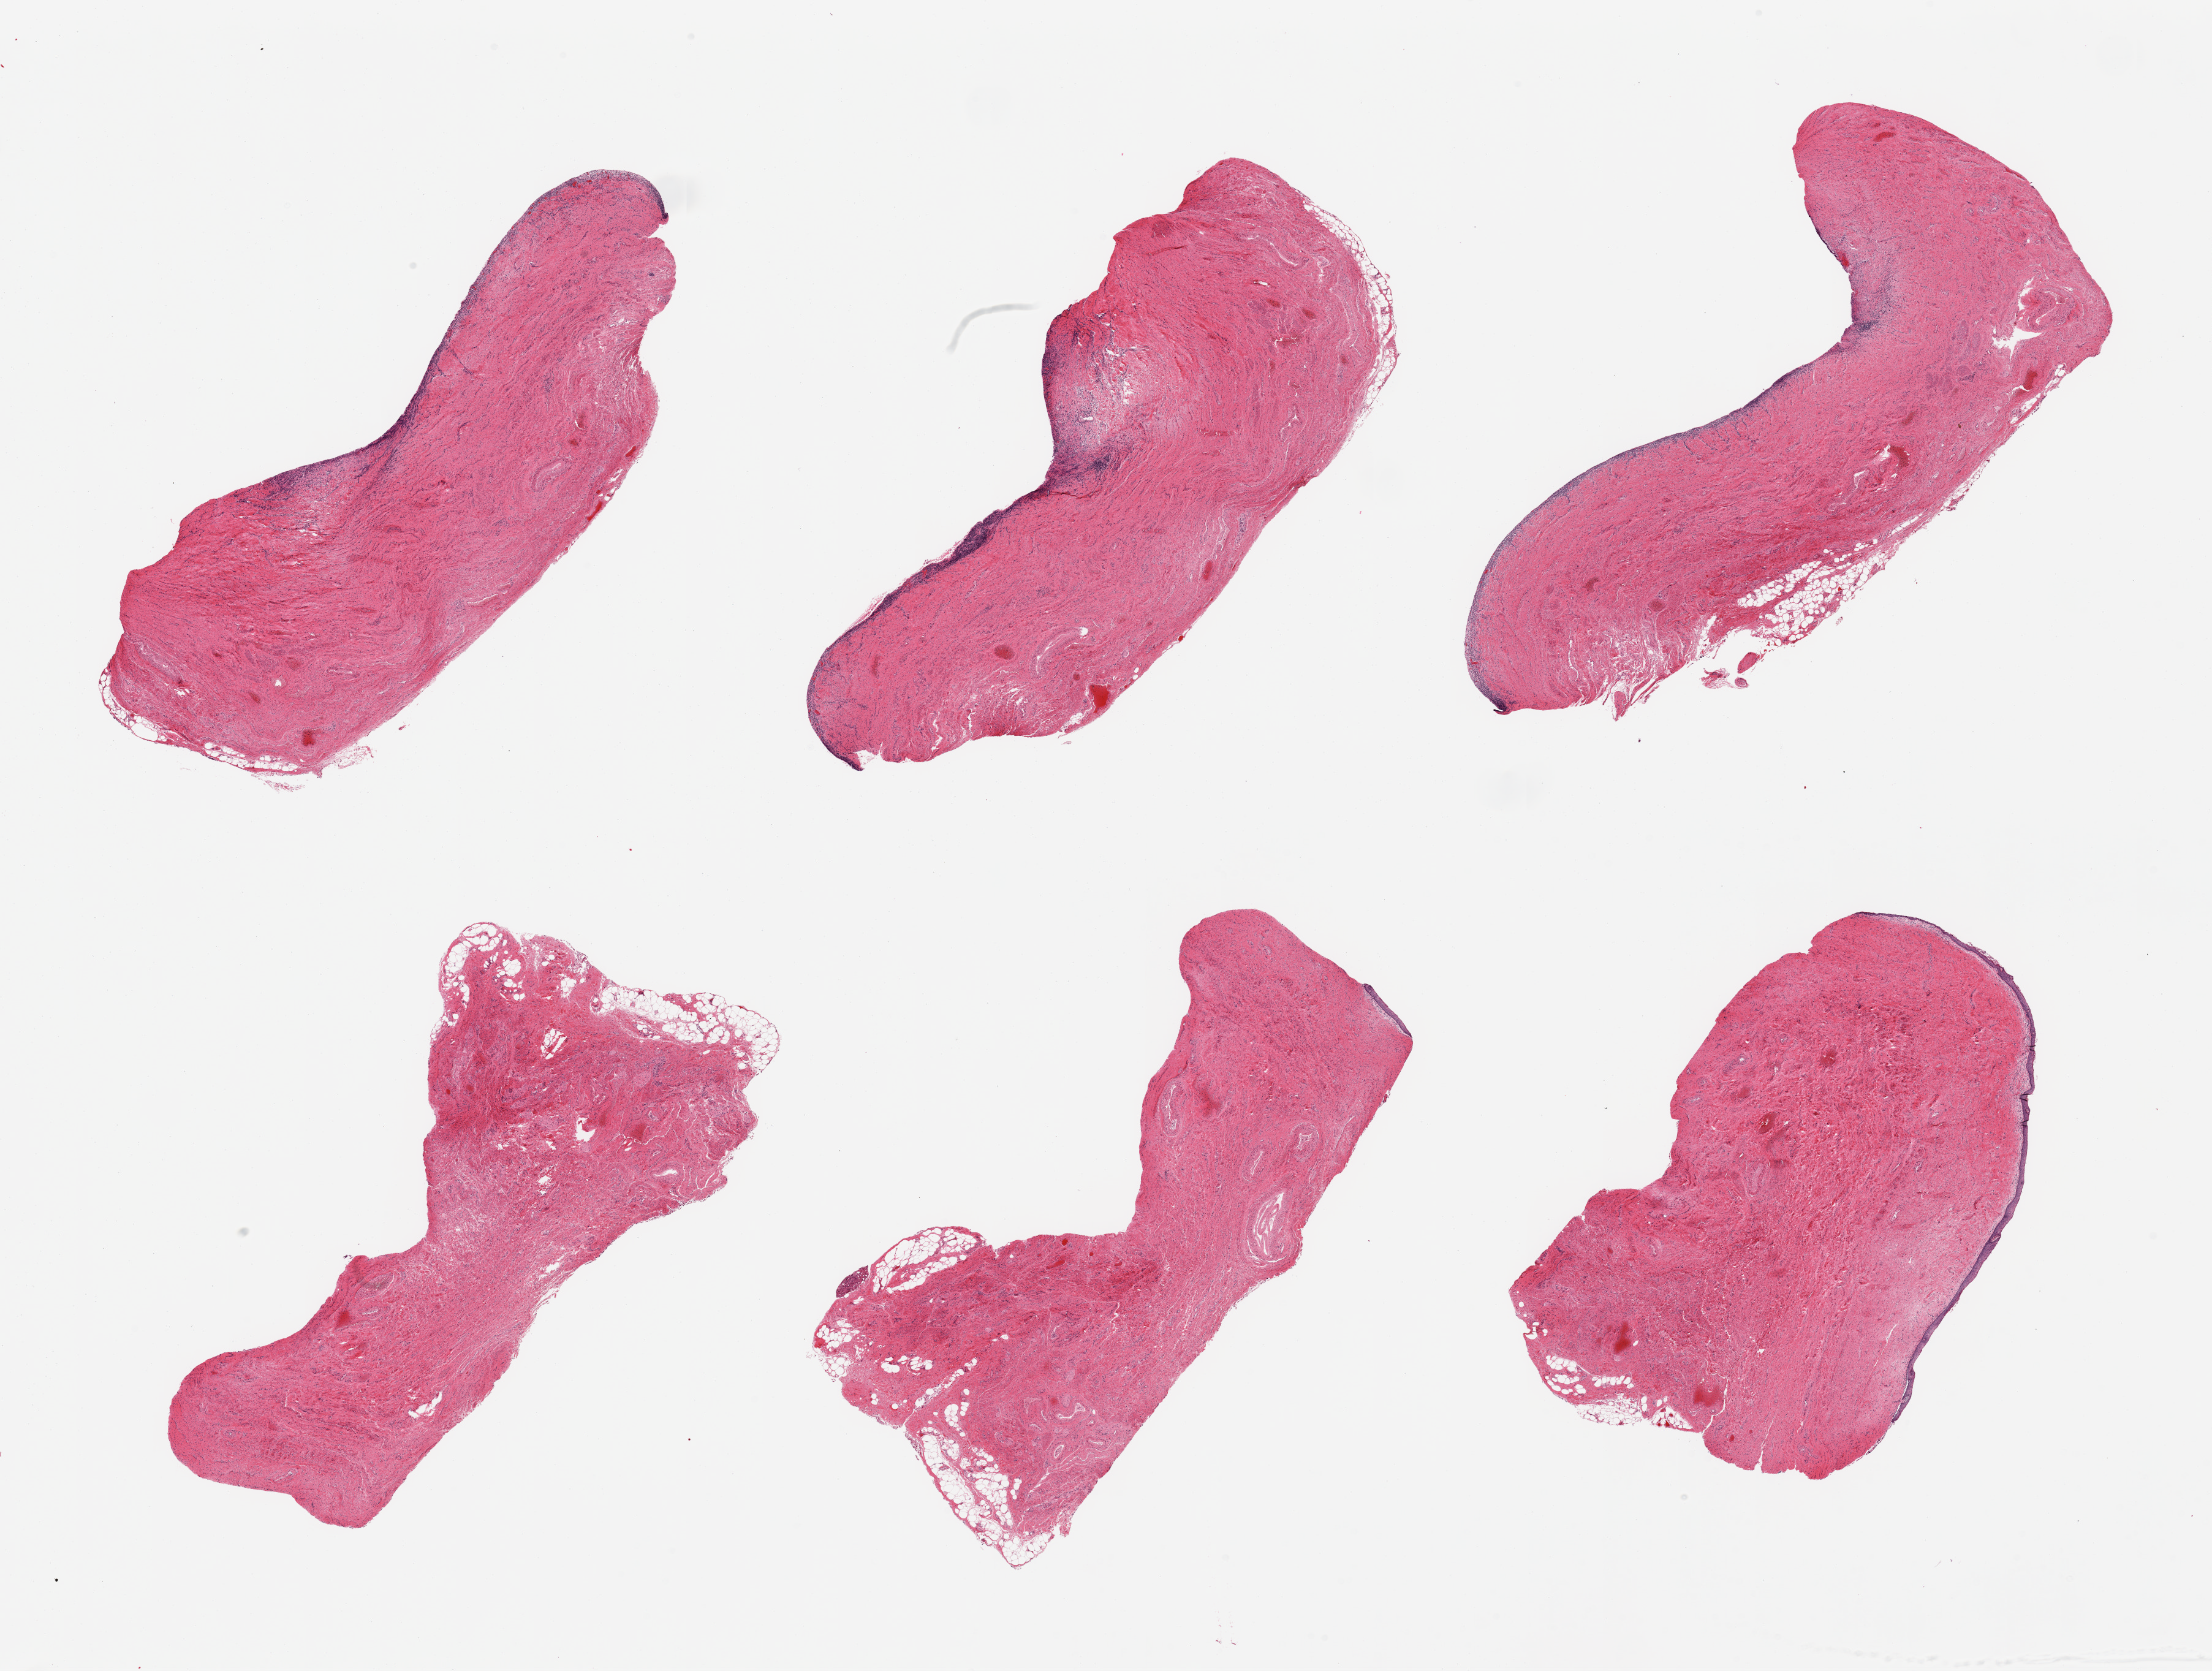
Haematoxylin and eosin whole-slide image, low-resolution overview of the scanned area, about 28.5 x 21.6 mm (from a 20x scan). PAXgene-fixed paraffin-embedded (PFPE) section. Section of vagina (target tissue). Tissue donor sample. Donor sex: female.
Reviewer comment on this tissue sample: 6 pieces; atrophic & sloughed mucosa; chronic inflammation.